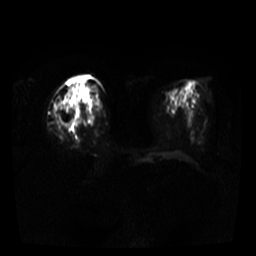
Breast MRI, one axial slice. Slice 14 of 37 in the series (ordered by position). Diffusion-weighted series; image 2 of 4 stored at this slice position (different b-values; order by instance number). 3 T. 5 mm slice thickness. 256 × 256 image matrix, field of view 320 × 320 mm. Female patient.
Outlined on this slice (outlined manually by an expert reader):
- tumour on diffusion-weighted imaging: bounding box <67,84,78,128> (left, top, right, bottom; pixels)